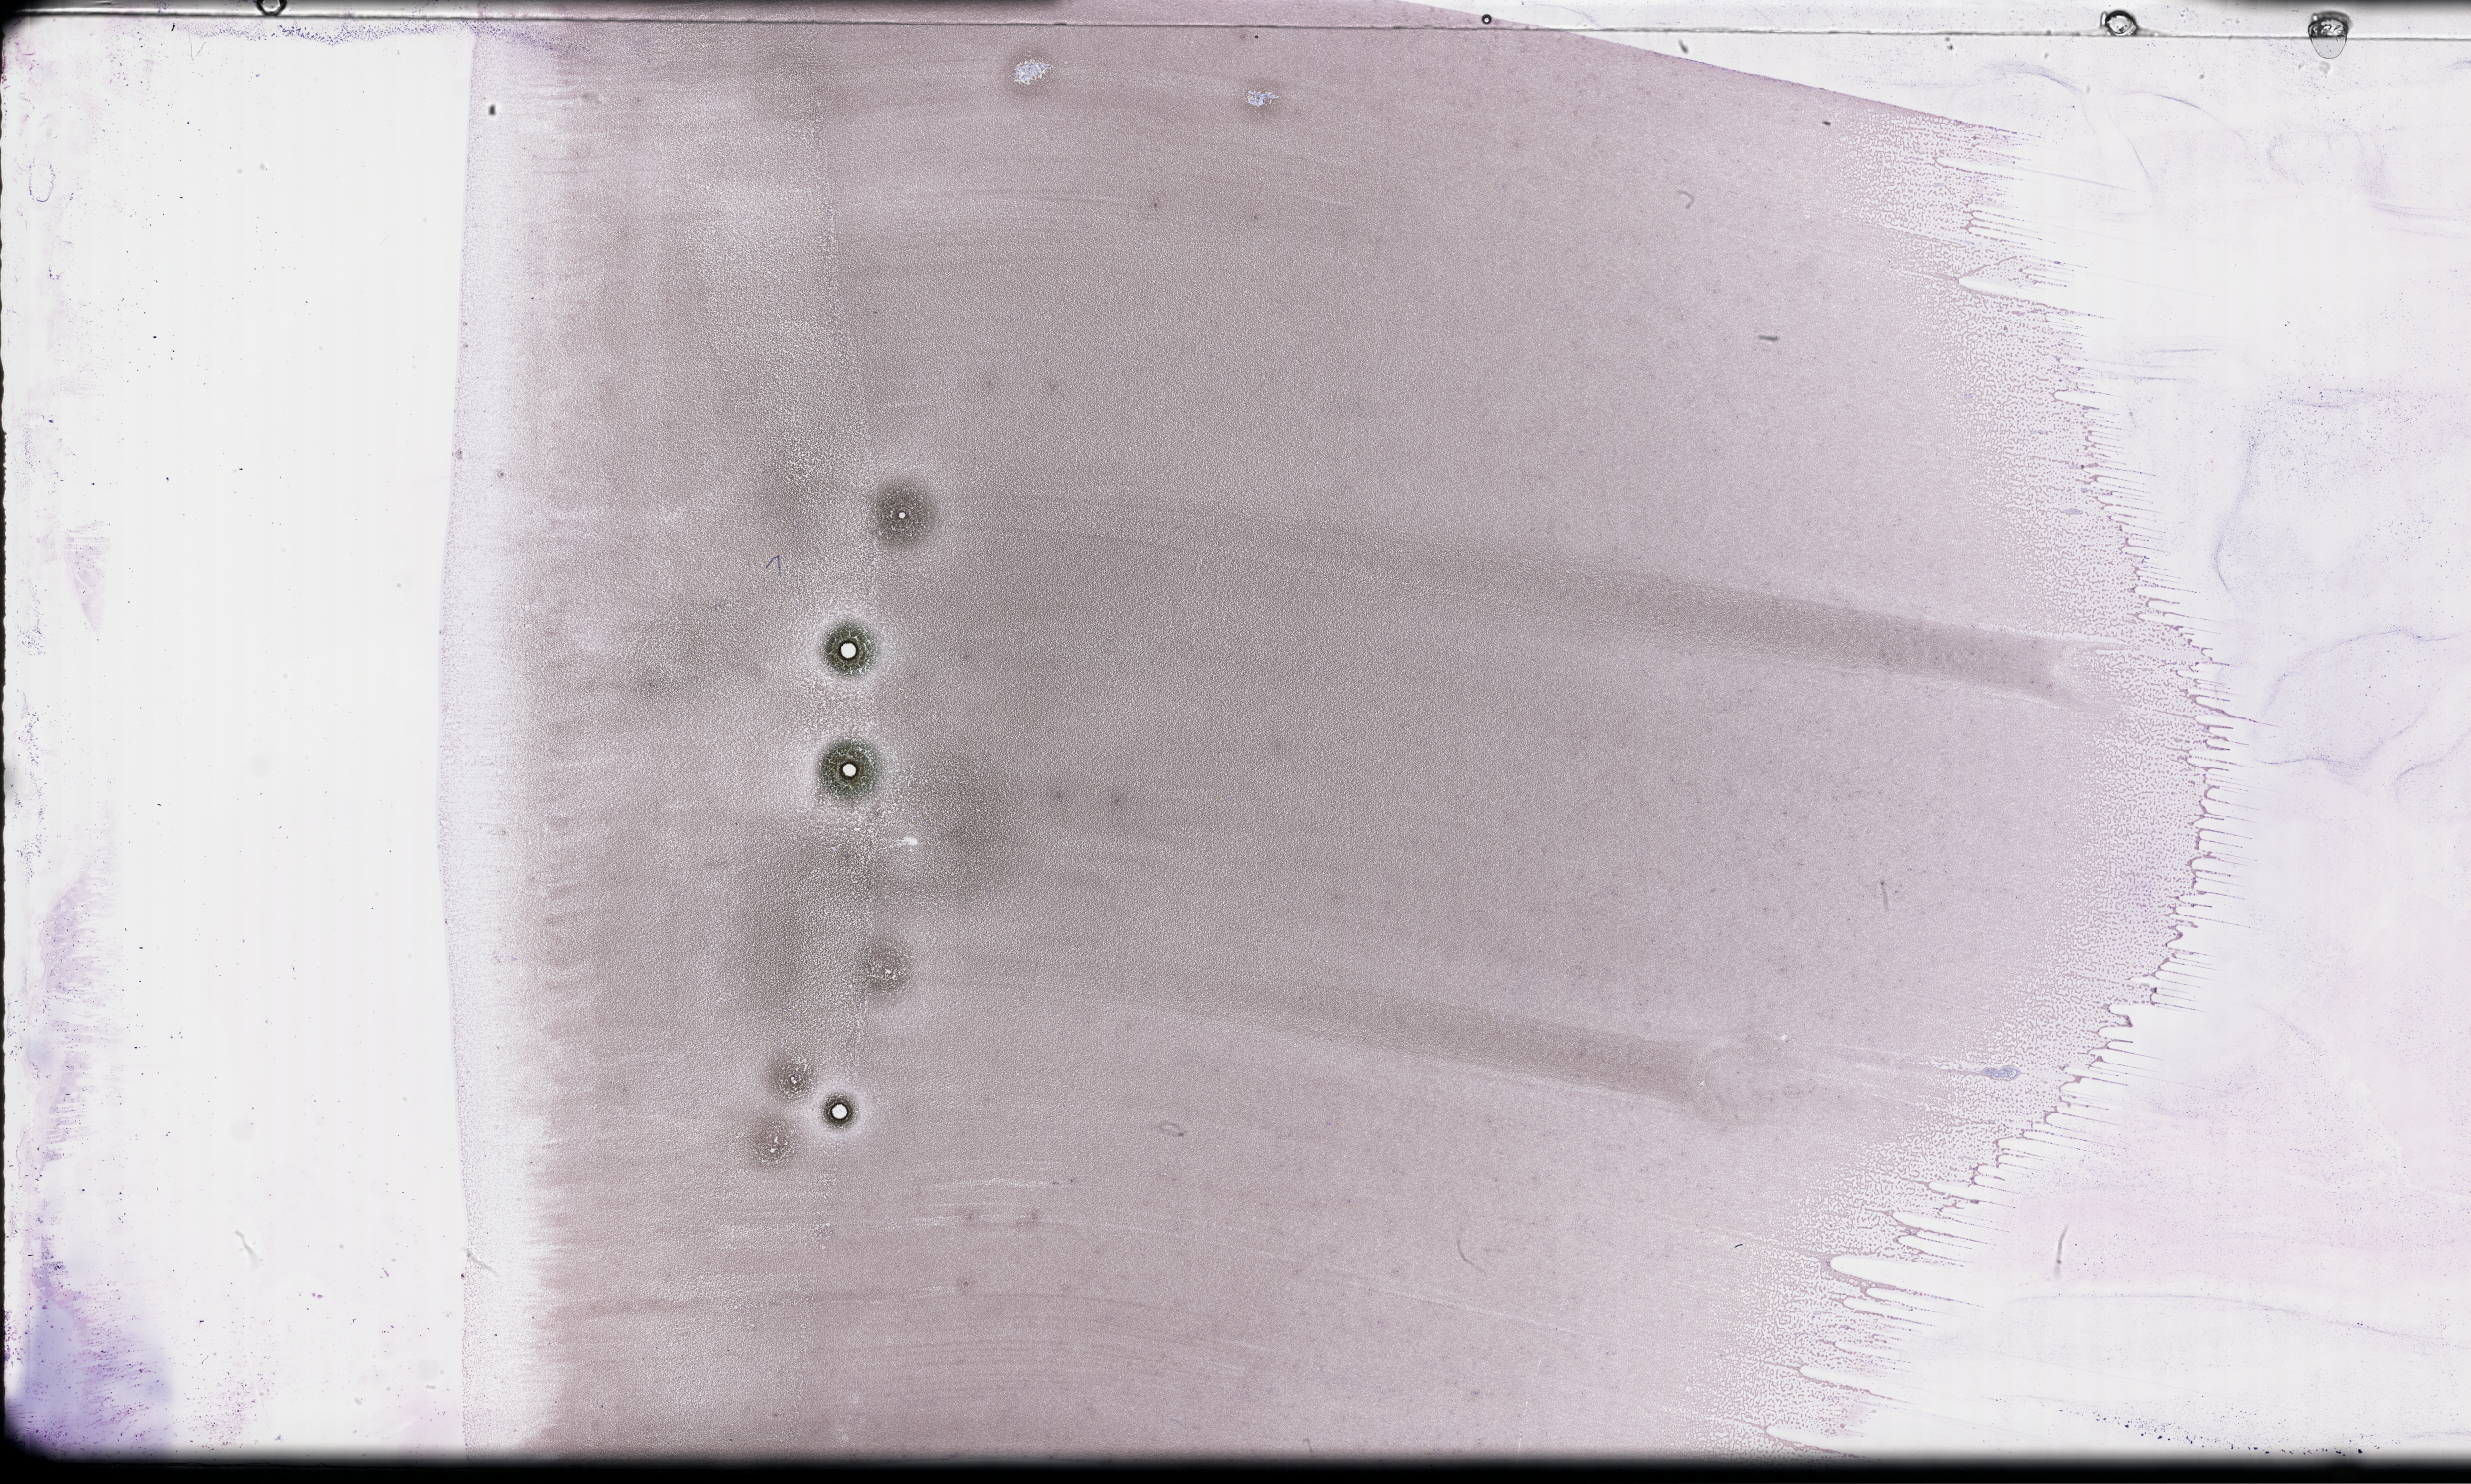
Wright–Giemsa-stained whole blood smear, whole-slide image, low-resolution overview of the scanned area, about 40.7 x 24.4 mm; specimen time point: collected post-treatment, no progression. Patient: female.
Patient diagnosis: Acute Myeloid Leukemia Not Otherwise Specified.